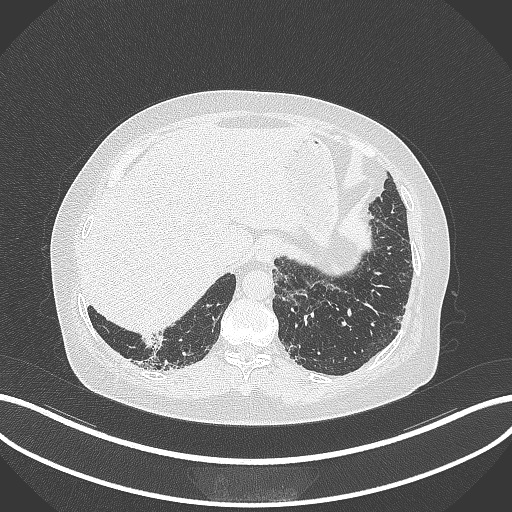
Chest CT, one axial slice. Position 12 of 296 along the scan axis. Reconstruction kernel B70f. Lung window (W 1500 / L -600 HU). 1 mm slice thickness. 512 × 512 image matrix, field of view 400 × 400 mm. Female patient, age 65 years. Case-level facts recorded for this patient, not image findings: clinical TNM (as recorded): T2b N1 M0; histopathological grade: G1.
Annotated regions visible in this slice (bounding box drawn by a radiologist):
- lung tumour (recorded histology: adenocarcinoma): bounding box [x1, y1, x2, y2] px = [139, 331, 171, 354]